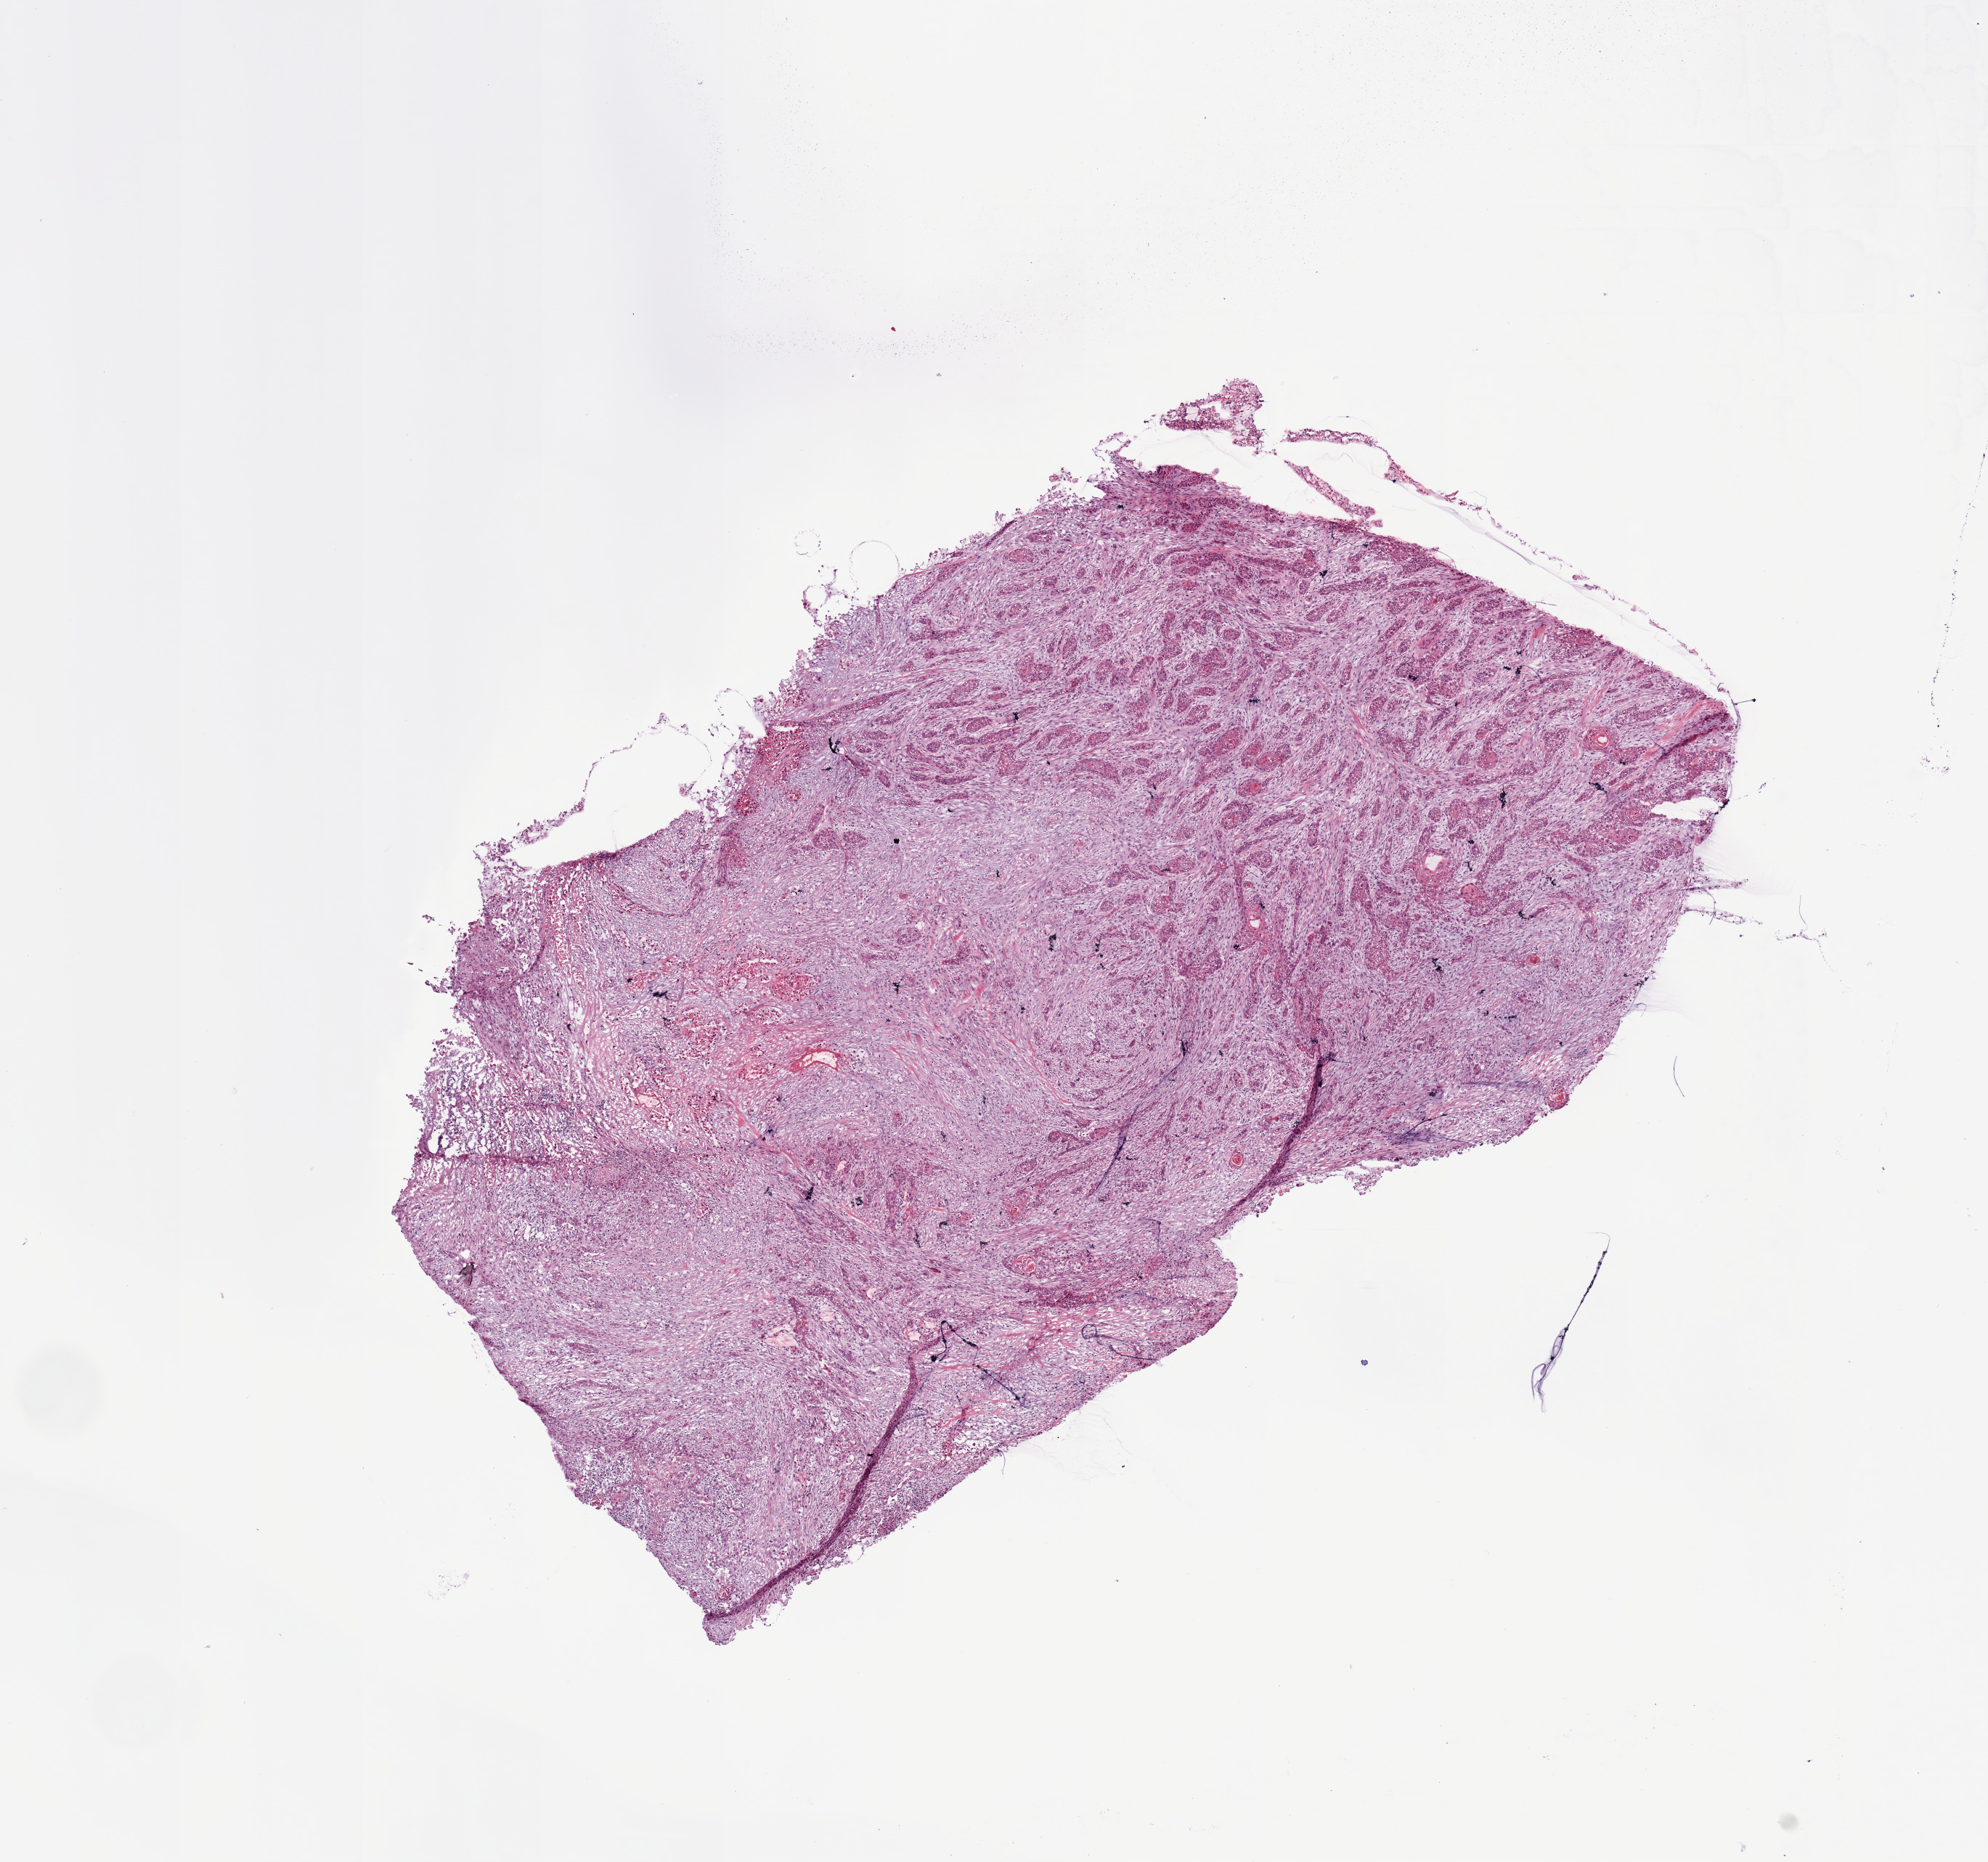
Digitized H&E tissue section (whole slide) — whole scanned area (about 10.8 x 10.1 mm, from a 20x scan) shown as a low-resolution overview; lung, tumour tissue. Patient: female, age 75 years.
Patient diagnosis (cohort enrolment): squamous cell carcinoma (lung). Primary tumour site (as recorded): right upper lobe.